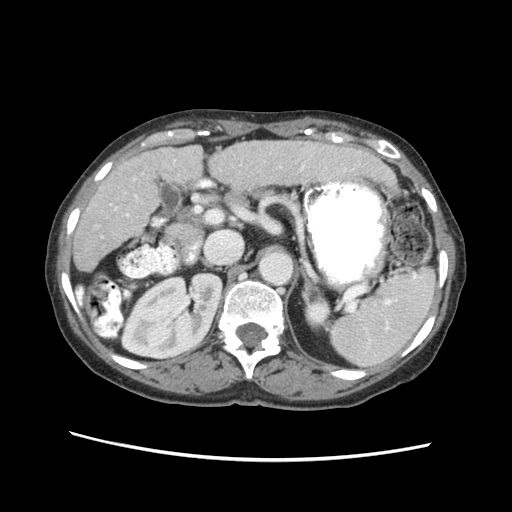
Contrast-enhanced abdominal CT (liver protocol), one axial slice. Slice 30 of 63 in the series (ordered by position). Reconstruction kernel STANDARD. Soft-tissue window (W 400 / L 40 HU). 512 × 512 image matrix, field of view 340 × 340 mm. From the clinical record (not read from this slice): diagnosis: hepatocellular carcinoma (patient treated with transarterial chemoembolisation; whether this scan precedes or follows treatment is not stated here); TNM stage (as recorded): Stage-I; Child-Pugh class: B; tumour differentiation: well differentiated.
Annotated regions visible in this slice (semi-automatically segmented with operator editing):
- liver parenchyma outside the tumour (the mass and vessels are separate outlines, so this box may not span the whole liver): box from (x=74, y=136) to (x=394, y=270) px
- liver vessels: (x=100, y=160)–(x=342, y=236)